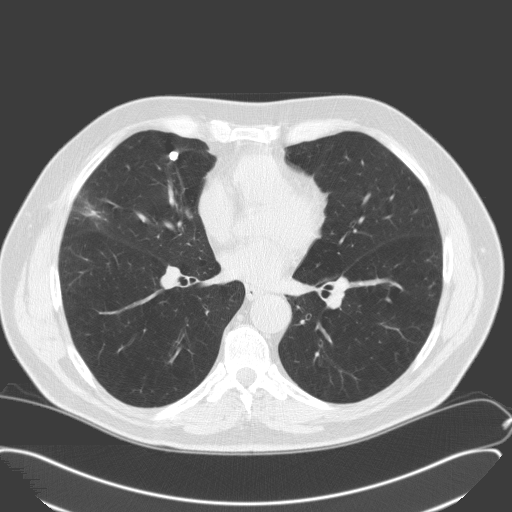
Axial slice from a low-dose chest CT screening exam. Second annual screen. Lung window (W 1500 / L -600 HU). 120 kVp. 512 × 512 image matrix, field of view 400 × 400 mm. Male, age 65 years at enrolment.
Expert reader's lesion annotation, box from (x=47, y=189) to (x=118, y=244) px. Screening reader's record for this exam: no non-calcified nodule ≥4 mm recorded. Official screen result: negative screen, minor abnormalities not suspicious for lung cancer.